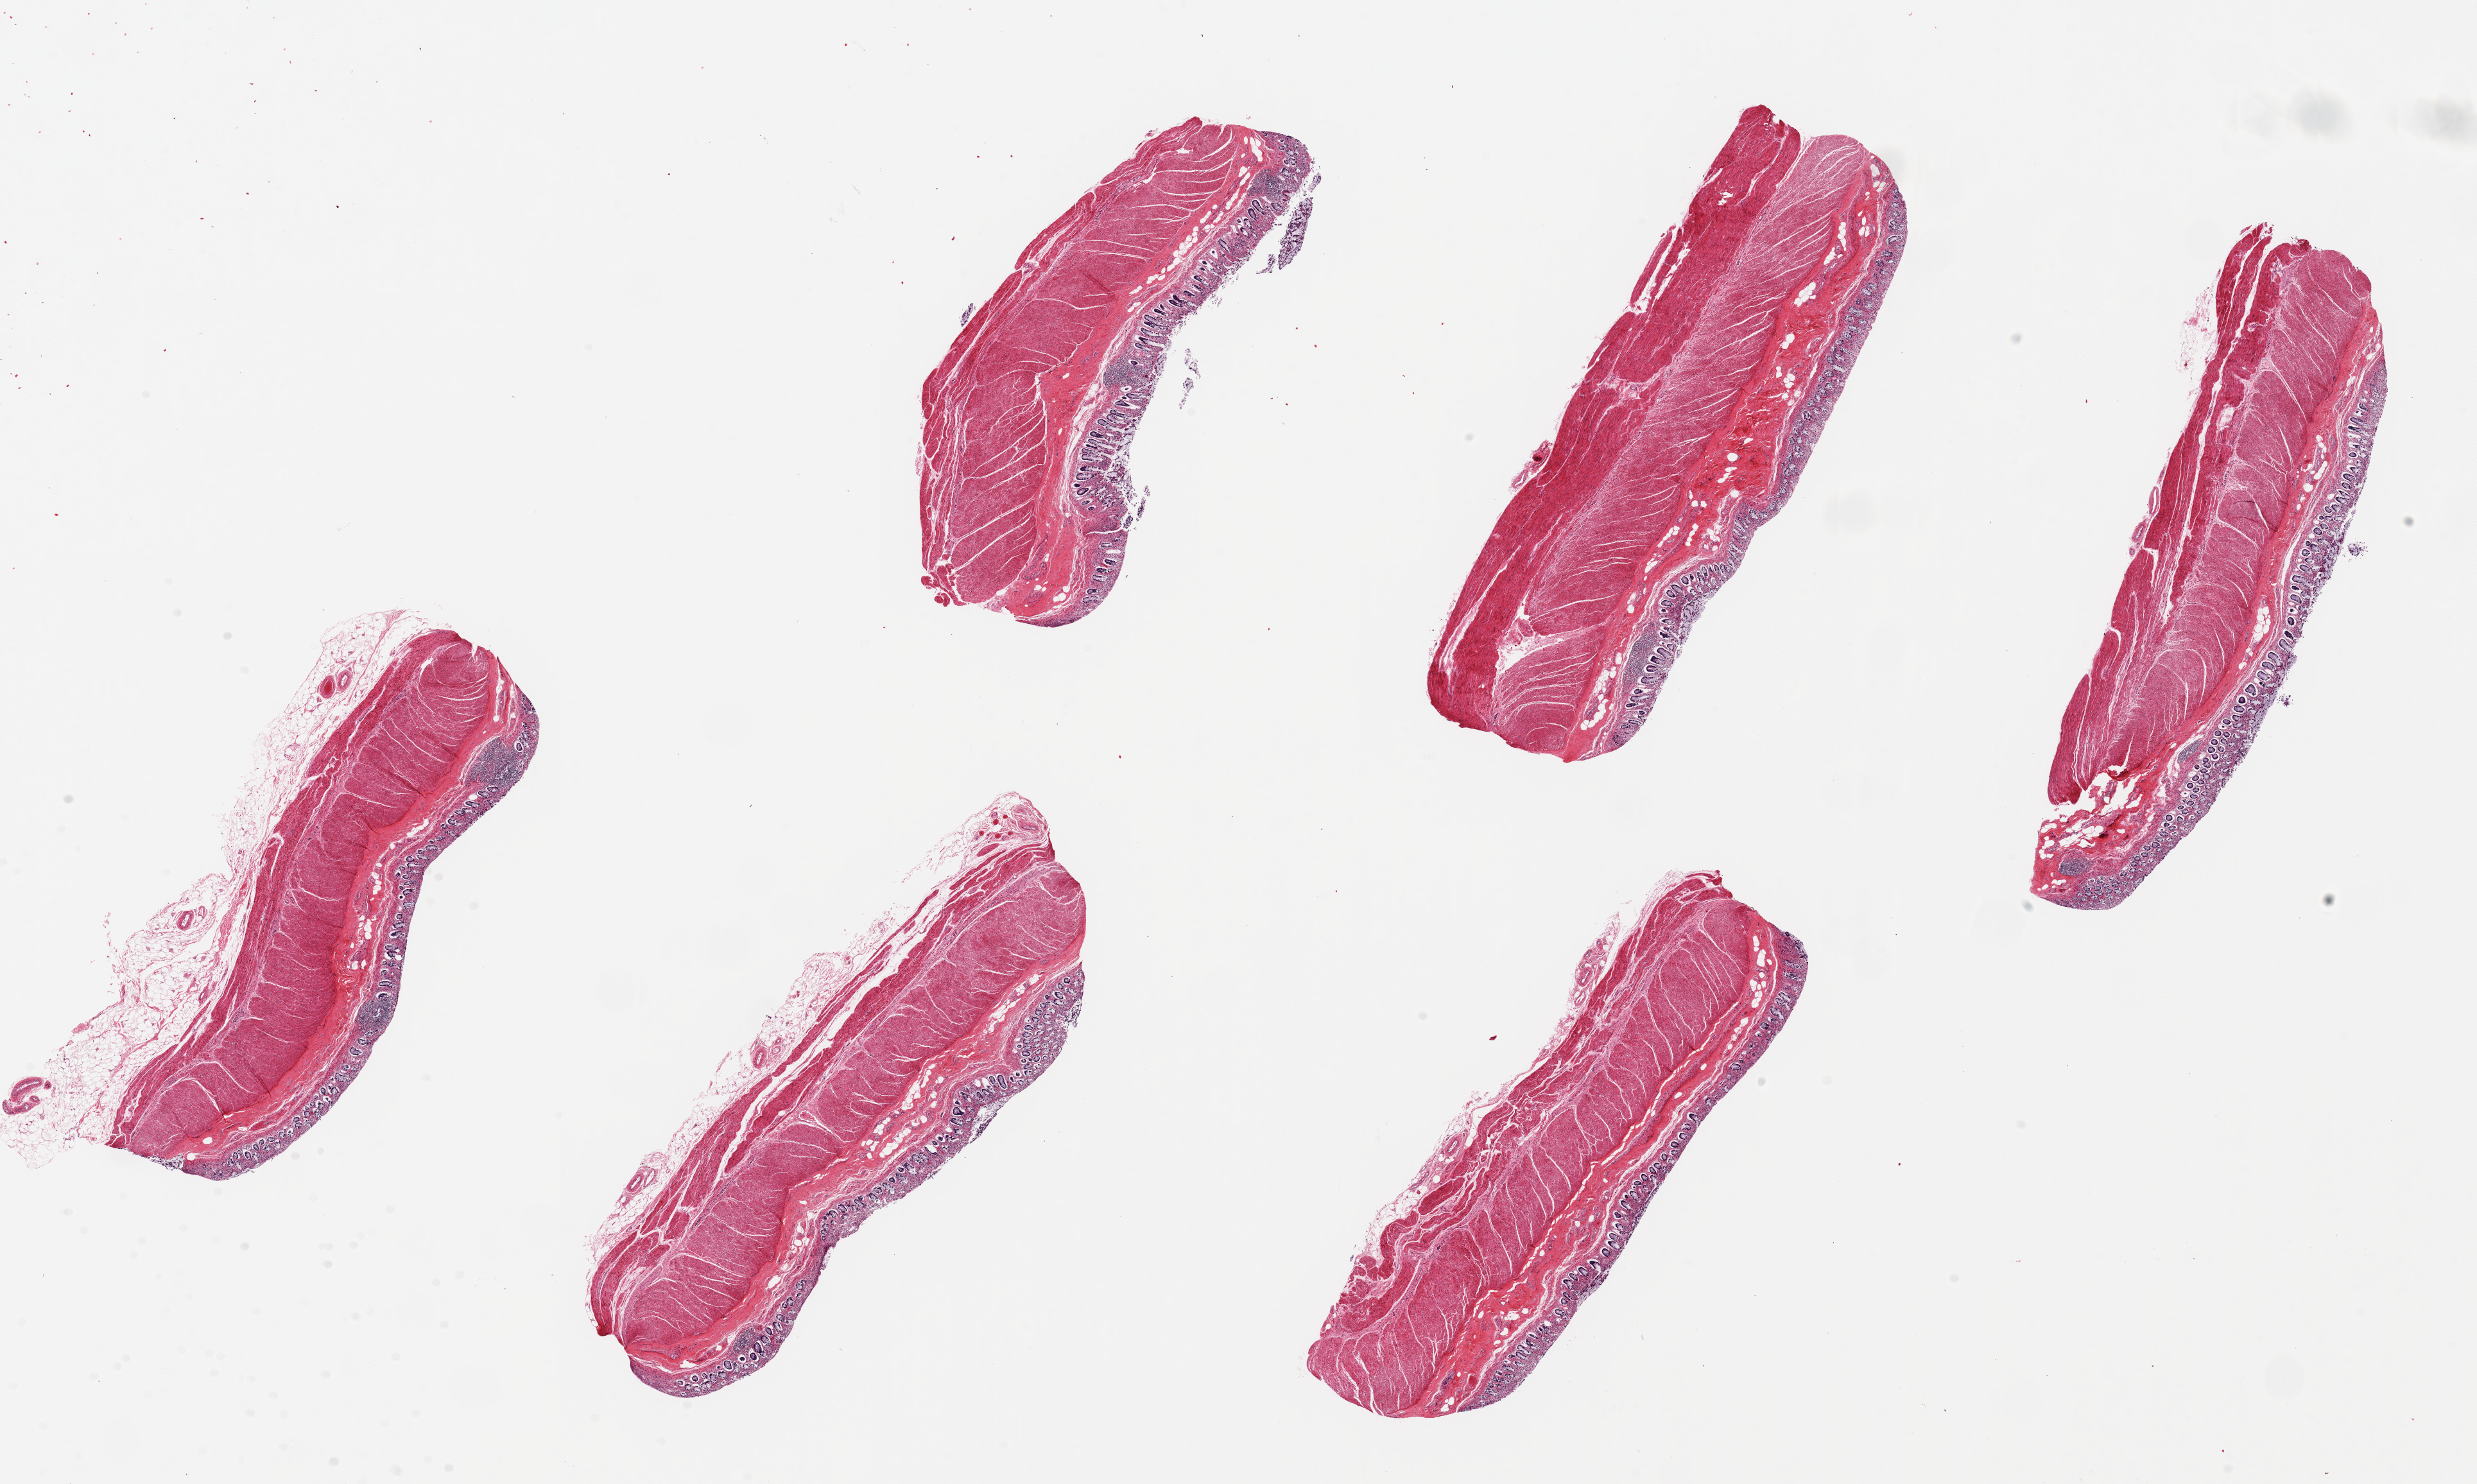
Whole-slide image, H&E stain — low-resolution overview of the scanned area, about 30.5 x 18.3 mm (acquisition: 20x scan); PAXgene-fixed, paraffin-embedded tissue; section of sigmoid colon (target tissue); tissue donor sample.
- review note (as recorded): 6 pieces ~8x2.5mm; muscularis propria is ~90% of specimens